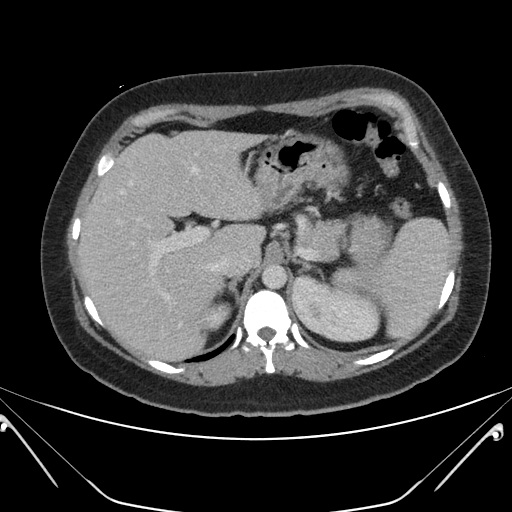
Contrast-enhanced abdominal CT, one axial slice; slice 133 of 168 in the series (ordered by position); 120 kVp; soft-tissue window (W 400 / L 40 HU); 512 × 512 image matrix, field of view 394 × 394 mm. Patient: female, 26 years. From the clinical record (not read from this slice): diagnosis: adrenocortical carcinoma; tumour side: left adrenal; tumour size at pathology: 28 cm; Ki-67 index: 20 %; stage (as recorded): 2.
Structures marked on this image (semi-automatically segmented with operator editing):
- mass: bounding box (x1, y1, x2, y2) in pixels: (352, 219, 388, 266)